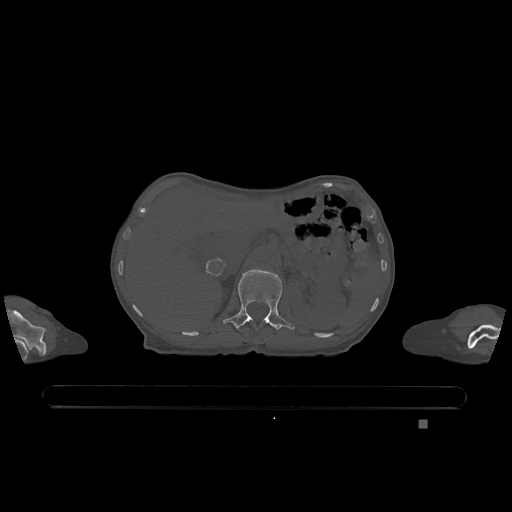
CT including the spine, one axial slice. Slice 480 of 1317 in the series (ordered by position). Bone window (W 1800 / L 400 HU). 0.5 mm slice thickness. 512 × 512 image matrix. Patient: female, 74 years. Case-level facts recorded for this patient, not image findings: primary cancer: lung; vertebrae with lytic lesions (as recorded): T1, T4, T5, T6, L4, L5.
Annotated regions visible in this slice (semi-automatic segmentation, software-assisted and operator-edited):
- L1 vertebra: box from (x=223, y=269) to (x=295, y=330) px